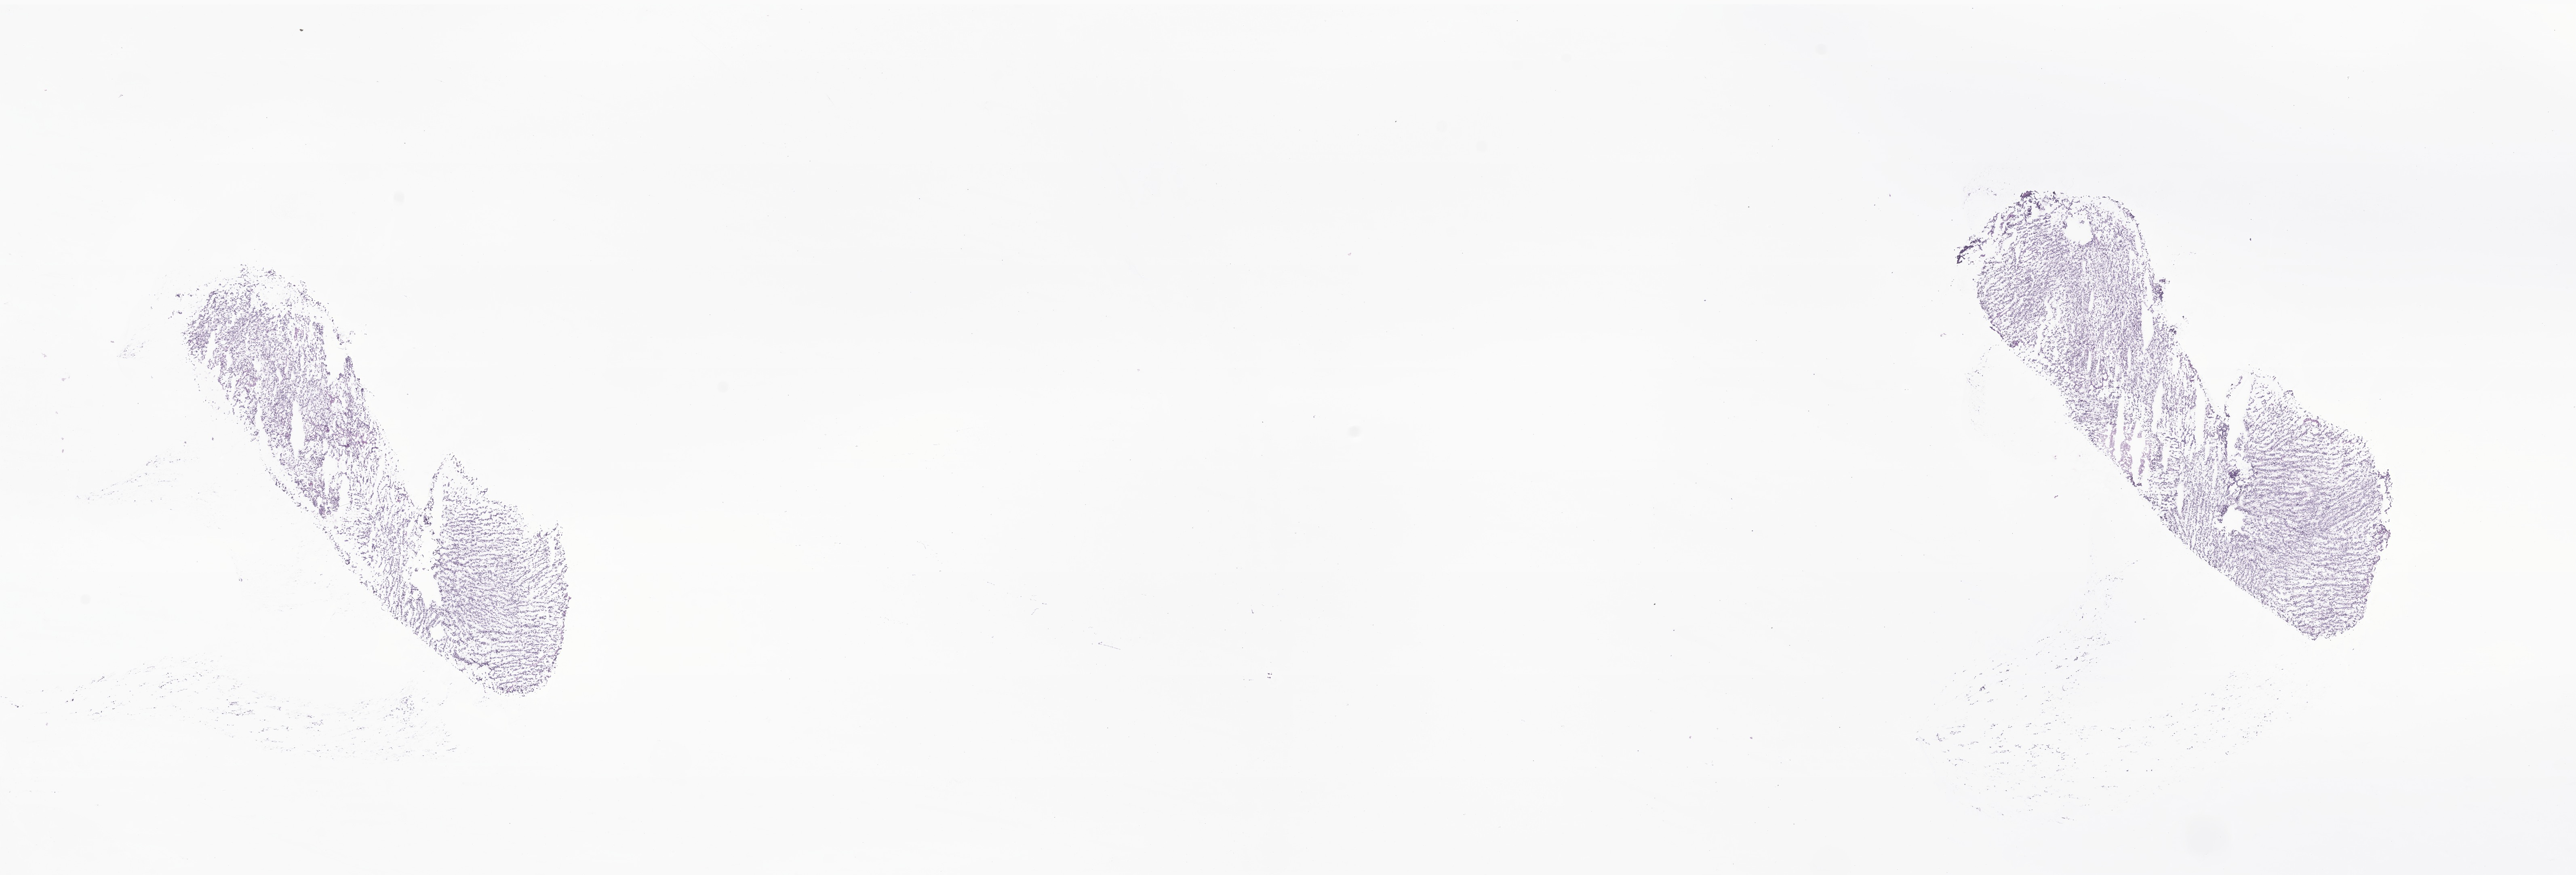
Digitized hematoxylin and eosin (H&E)-stained section of tumor tissue from the brain, shown as a low-resolution overview of the whole scanned area (about 26.9 x 9.1 mm). Frozen section. Male patient, age 82 months (6 years 10 months).
Diagnosis (ICD-O-3 morphology term): Medulloblastoma, NOS.